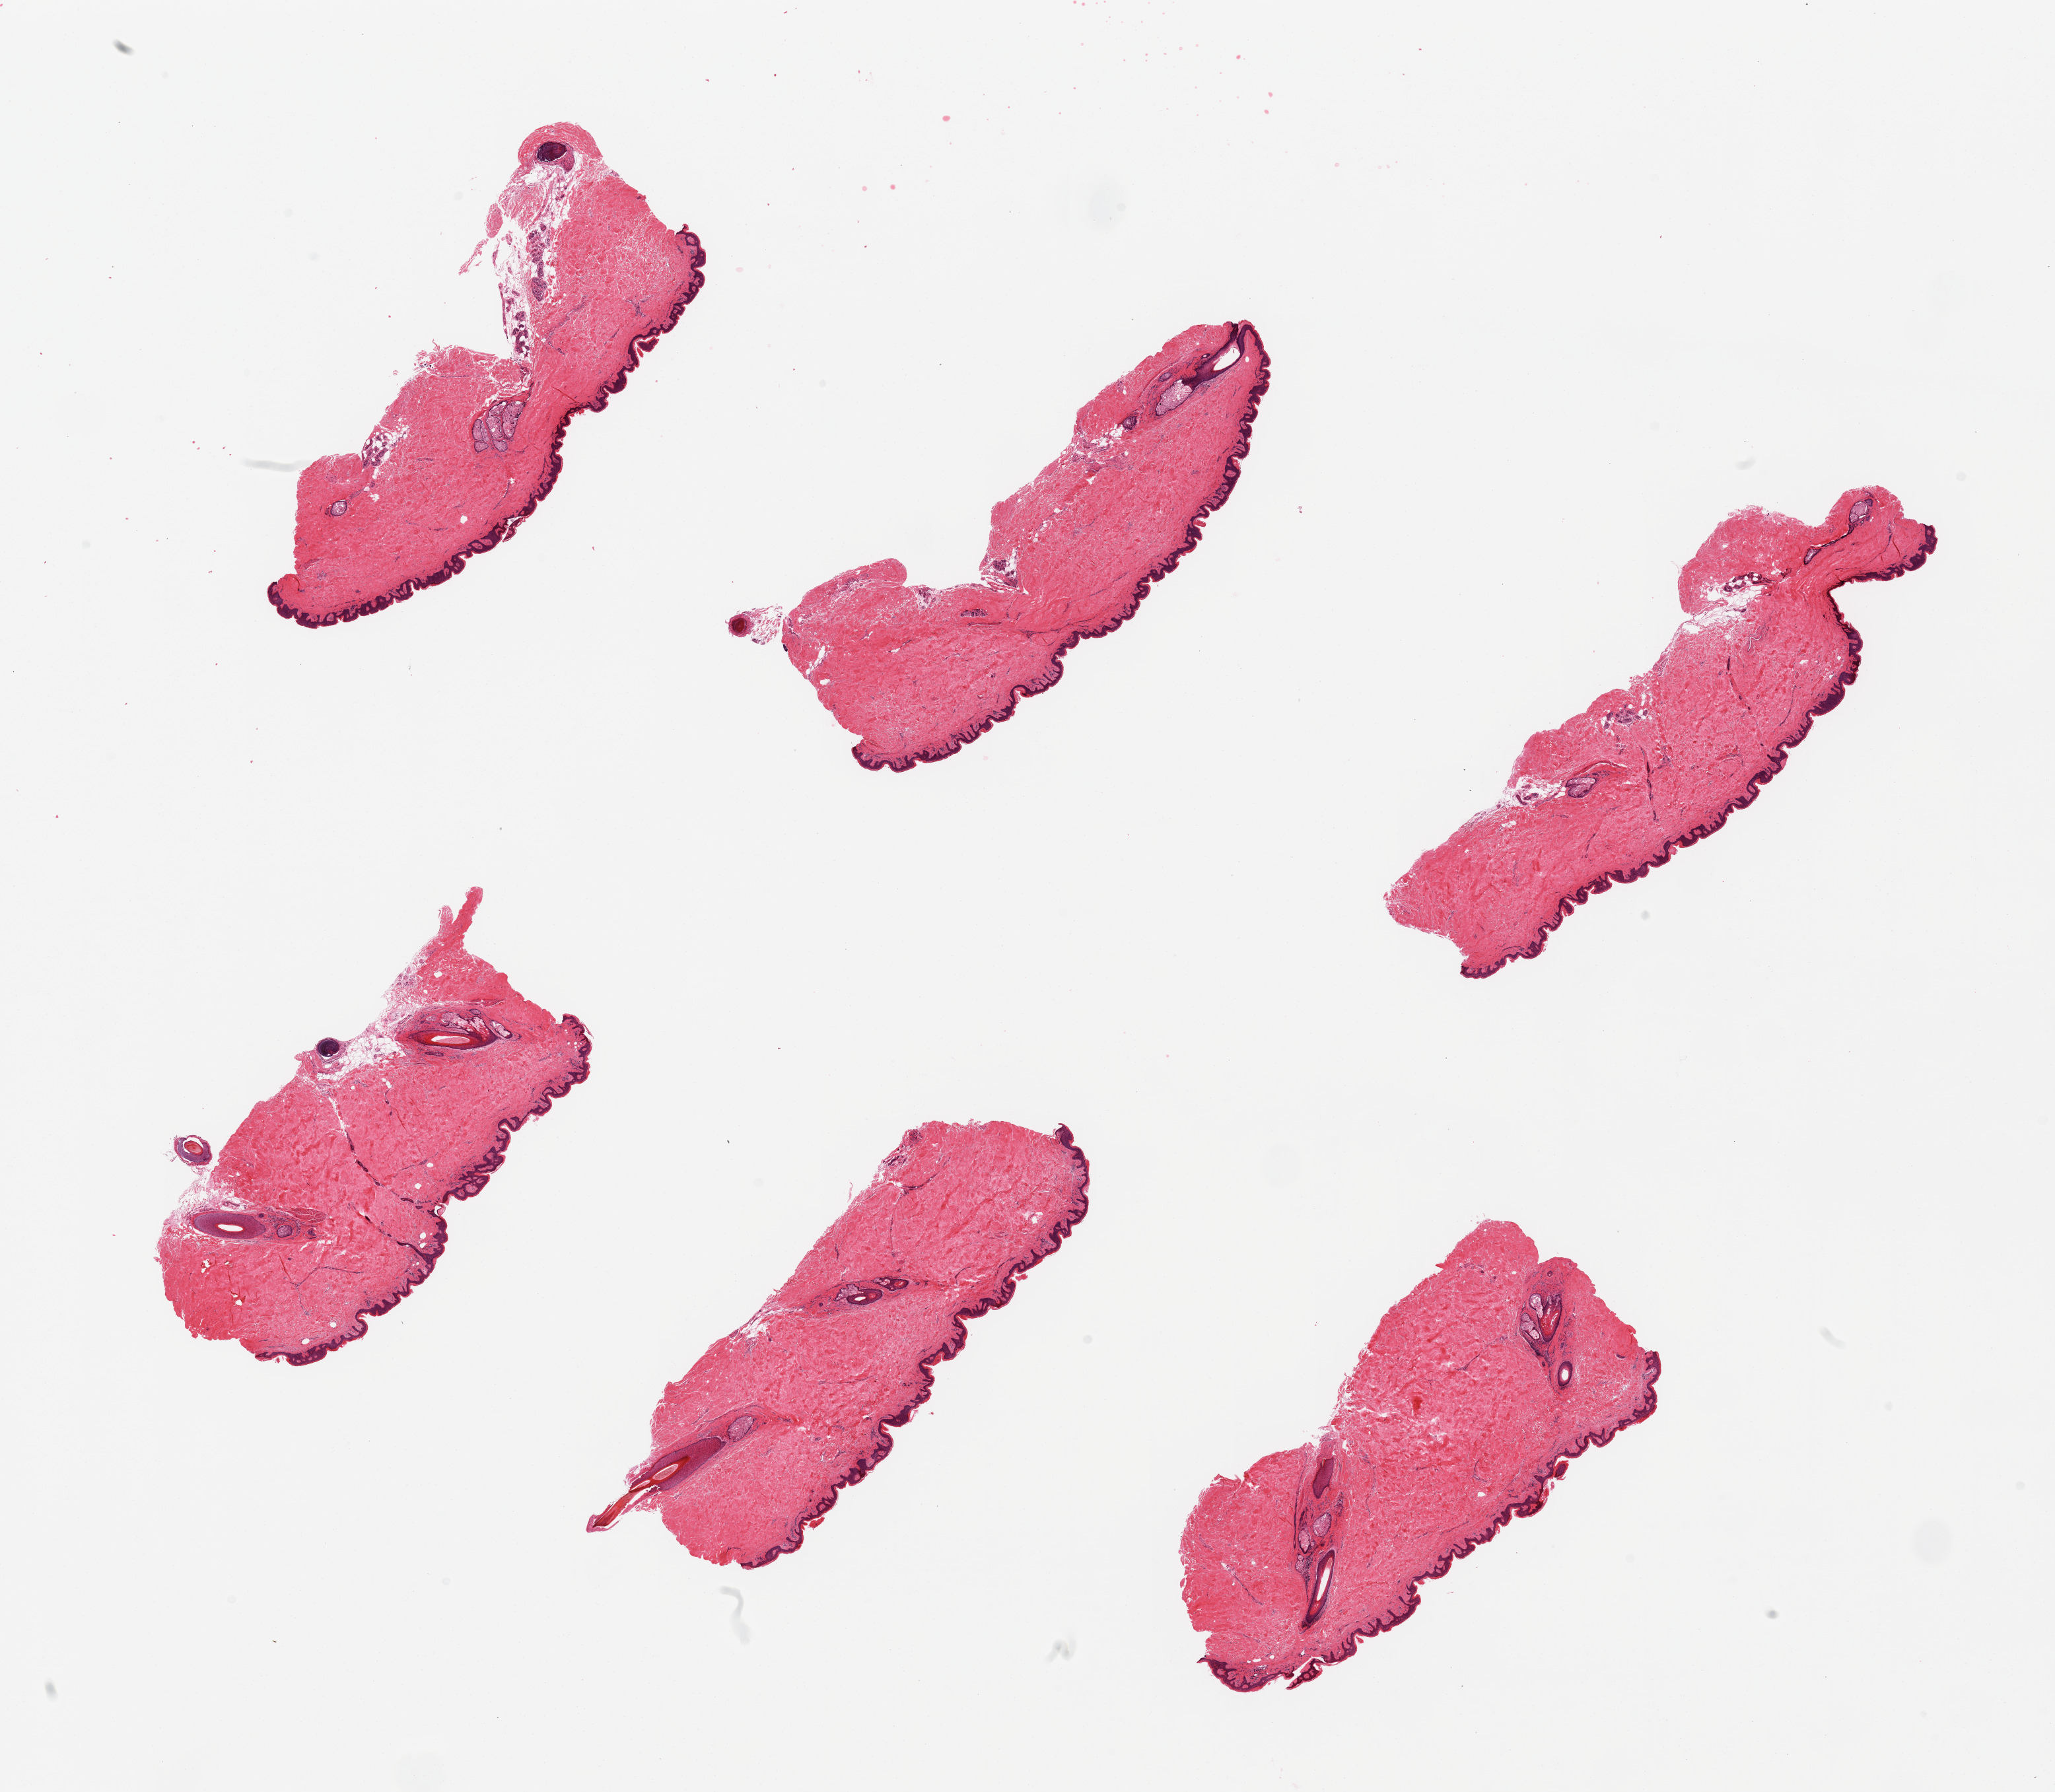
Haematoxylin and eosin whole-slide image, brightfield, whole scanned area (about 24.6 x 21.5 mm) shown as a low-resolution overview; PAXgene-fixed, paraffin-embedded tissue; sampled site (target tissue): skin of suprapubic region; donor tissue sample. Donor: male.
* review note (as recorded): 6 pieces; up to 2 hairs per piece